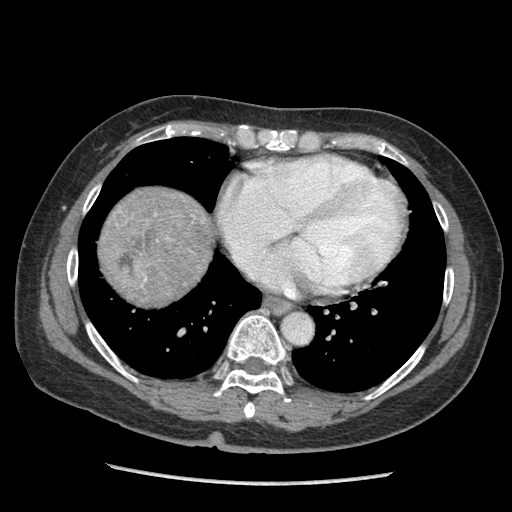
Contrast-enhanced abdominal CT (liver protocol), one axial slice; slice 93 of 105 in the series (ordered by position); soft-tissue window (W 400 / L 40 HU); 2.5 mm slice thickness; 512 × 512 image matrix, field of view 340 × 340 mm. From the clinical record (not read from this slice): diagnosis: hepatocellular carcinoma (patient treated with transarterial chemoembolisation; whether this scan precedes or follows treatment is not stated here); TNM stage (as recorded): Stage-I; Child-Pugh class: A; tumour differentiation: moderately differentiated; tumour nodularity: uninodular.
Annotated regions visible in this slice (semi-automatic segmentation, software-assisted and operator-edited):
- liver parenchyma outside the tumour (the mass and vessels are separate outlines, so this box may not span the whole liver): box from (x=100, y=186) to (x=204, y=255) px
- mass: (x=100, y=187)–(x=215, y=308)